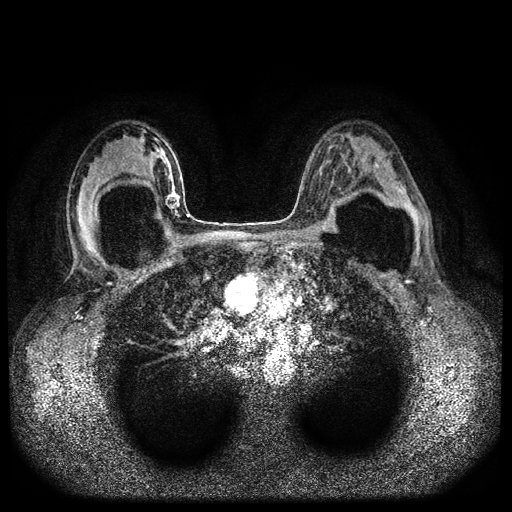
Breast MRI (dynamic contrast-enhanced, multi-phase), one axial slice; slice 58 of 116 in the series (ordered by position); dynamic contrast-enhanced series, time point 2 of 5 at this slice position (early post-contrast); 1.5 T; TE 2.6 ms, TR 5.4 ms; 2 mm slice thickness; 512 × 512 image matrix. Patient: female, 42 years.
Outlined on this slice (semi-automatically segmented with operator editing):
- breast lesion (labelled 'tumour' in the annotation; benign lesions carry a separate 'benign' label): bounding box (x1, y1, x2, y2) in pixels: (164, 191, 181, 212)